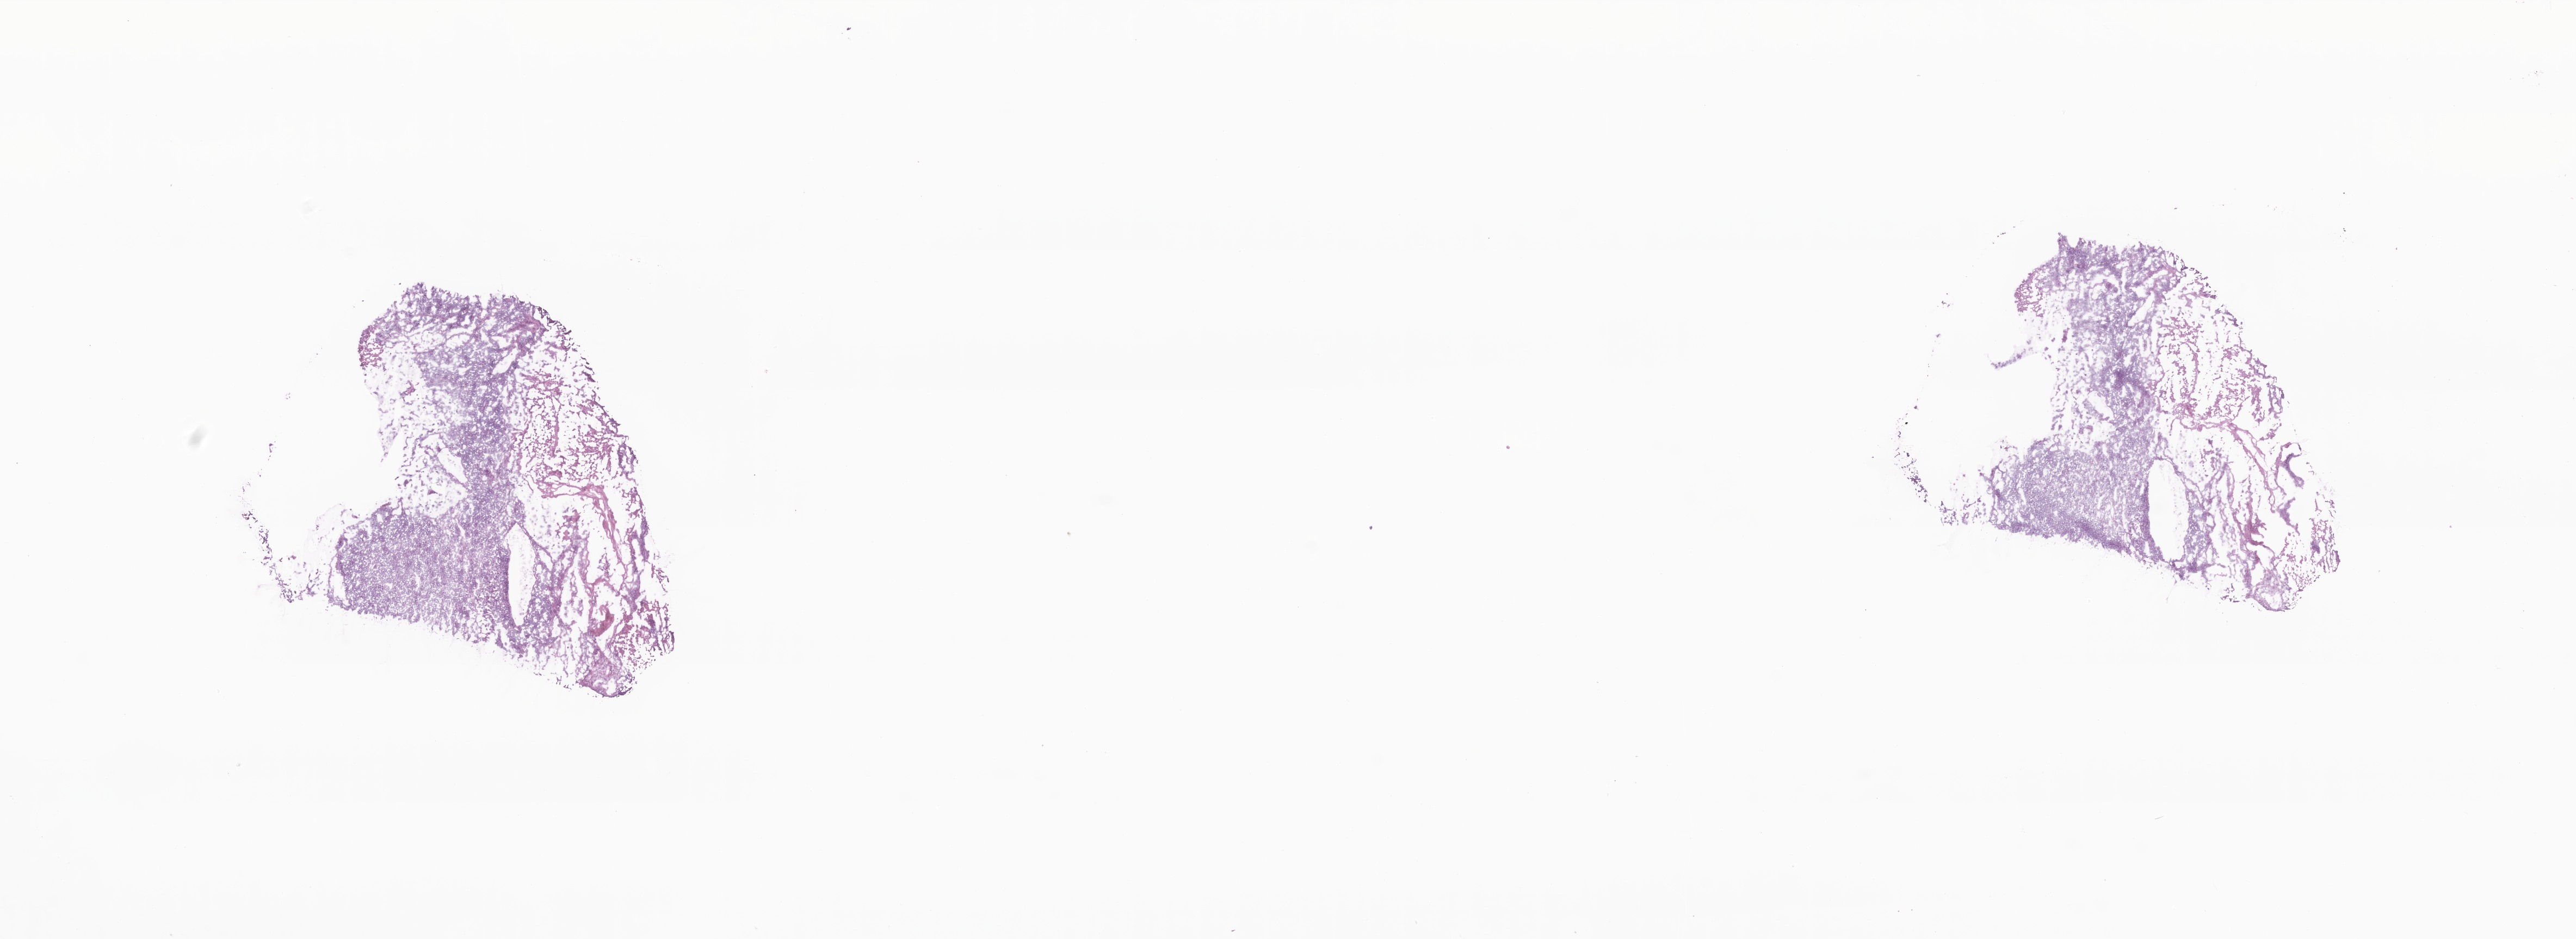
Whole-slide image, haematoxylin and eosin stain, low-resolution overview of the scanned area, about 20.0 x 7.3 mm, frozen section, specimen: primary tumor, anatomic site: body of uterus. Female patient. Tumor grade: G3 (poorly differentiated). Slide review estimates, as recorded: tumor cells 80%, tumor nuclei 80%, stromal cells 10%, necrosis 10%, normal cells 0%. Infiltration values recorded for this section: lymphocyte infiltration 3%, monocyte infiltration 1%, neutrophil infiltration 3%.
Diagnosis: Carcinoma, undifferentiated, NOS. AJCC pathologic stage: Stage IA.